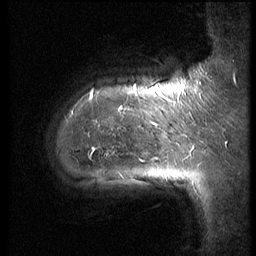
Breast MRI (dynamic contrast-enhanced), one sagittal slice; position 8 of 62 along the scan axis; 3 images stored at this slice position (order not interpretable as contrast timing); 1.5 T; TE 4.2 ms, TR 9 ms; 2.5 mm slice thickness; 256 × 256 image matrix. Female patient, age 39 years. Case-level facts recorded for this patient, not image findings: setting: breast cancer imaged before/during neoadjuvant chemotherapy; receptor status: HER2-positive.
Structures marked on this image (semi-automatically segmented with operator editing):
- analysis volume of interest (the breast-tissue region the enhancement analysis was run in; not a lesion): box from (x=40, y=64) to (x=171, y=220) px
- tumour enhancement mask (voxels above the 140 % enhancement threshold inside the analysis volume of interest): (x=93, y=89)–(x=159, y=148)